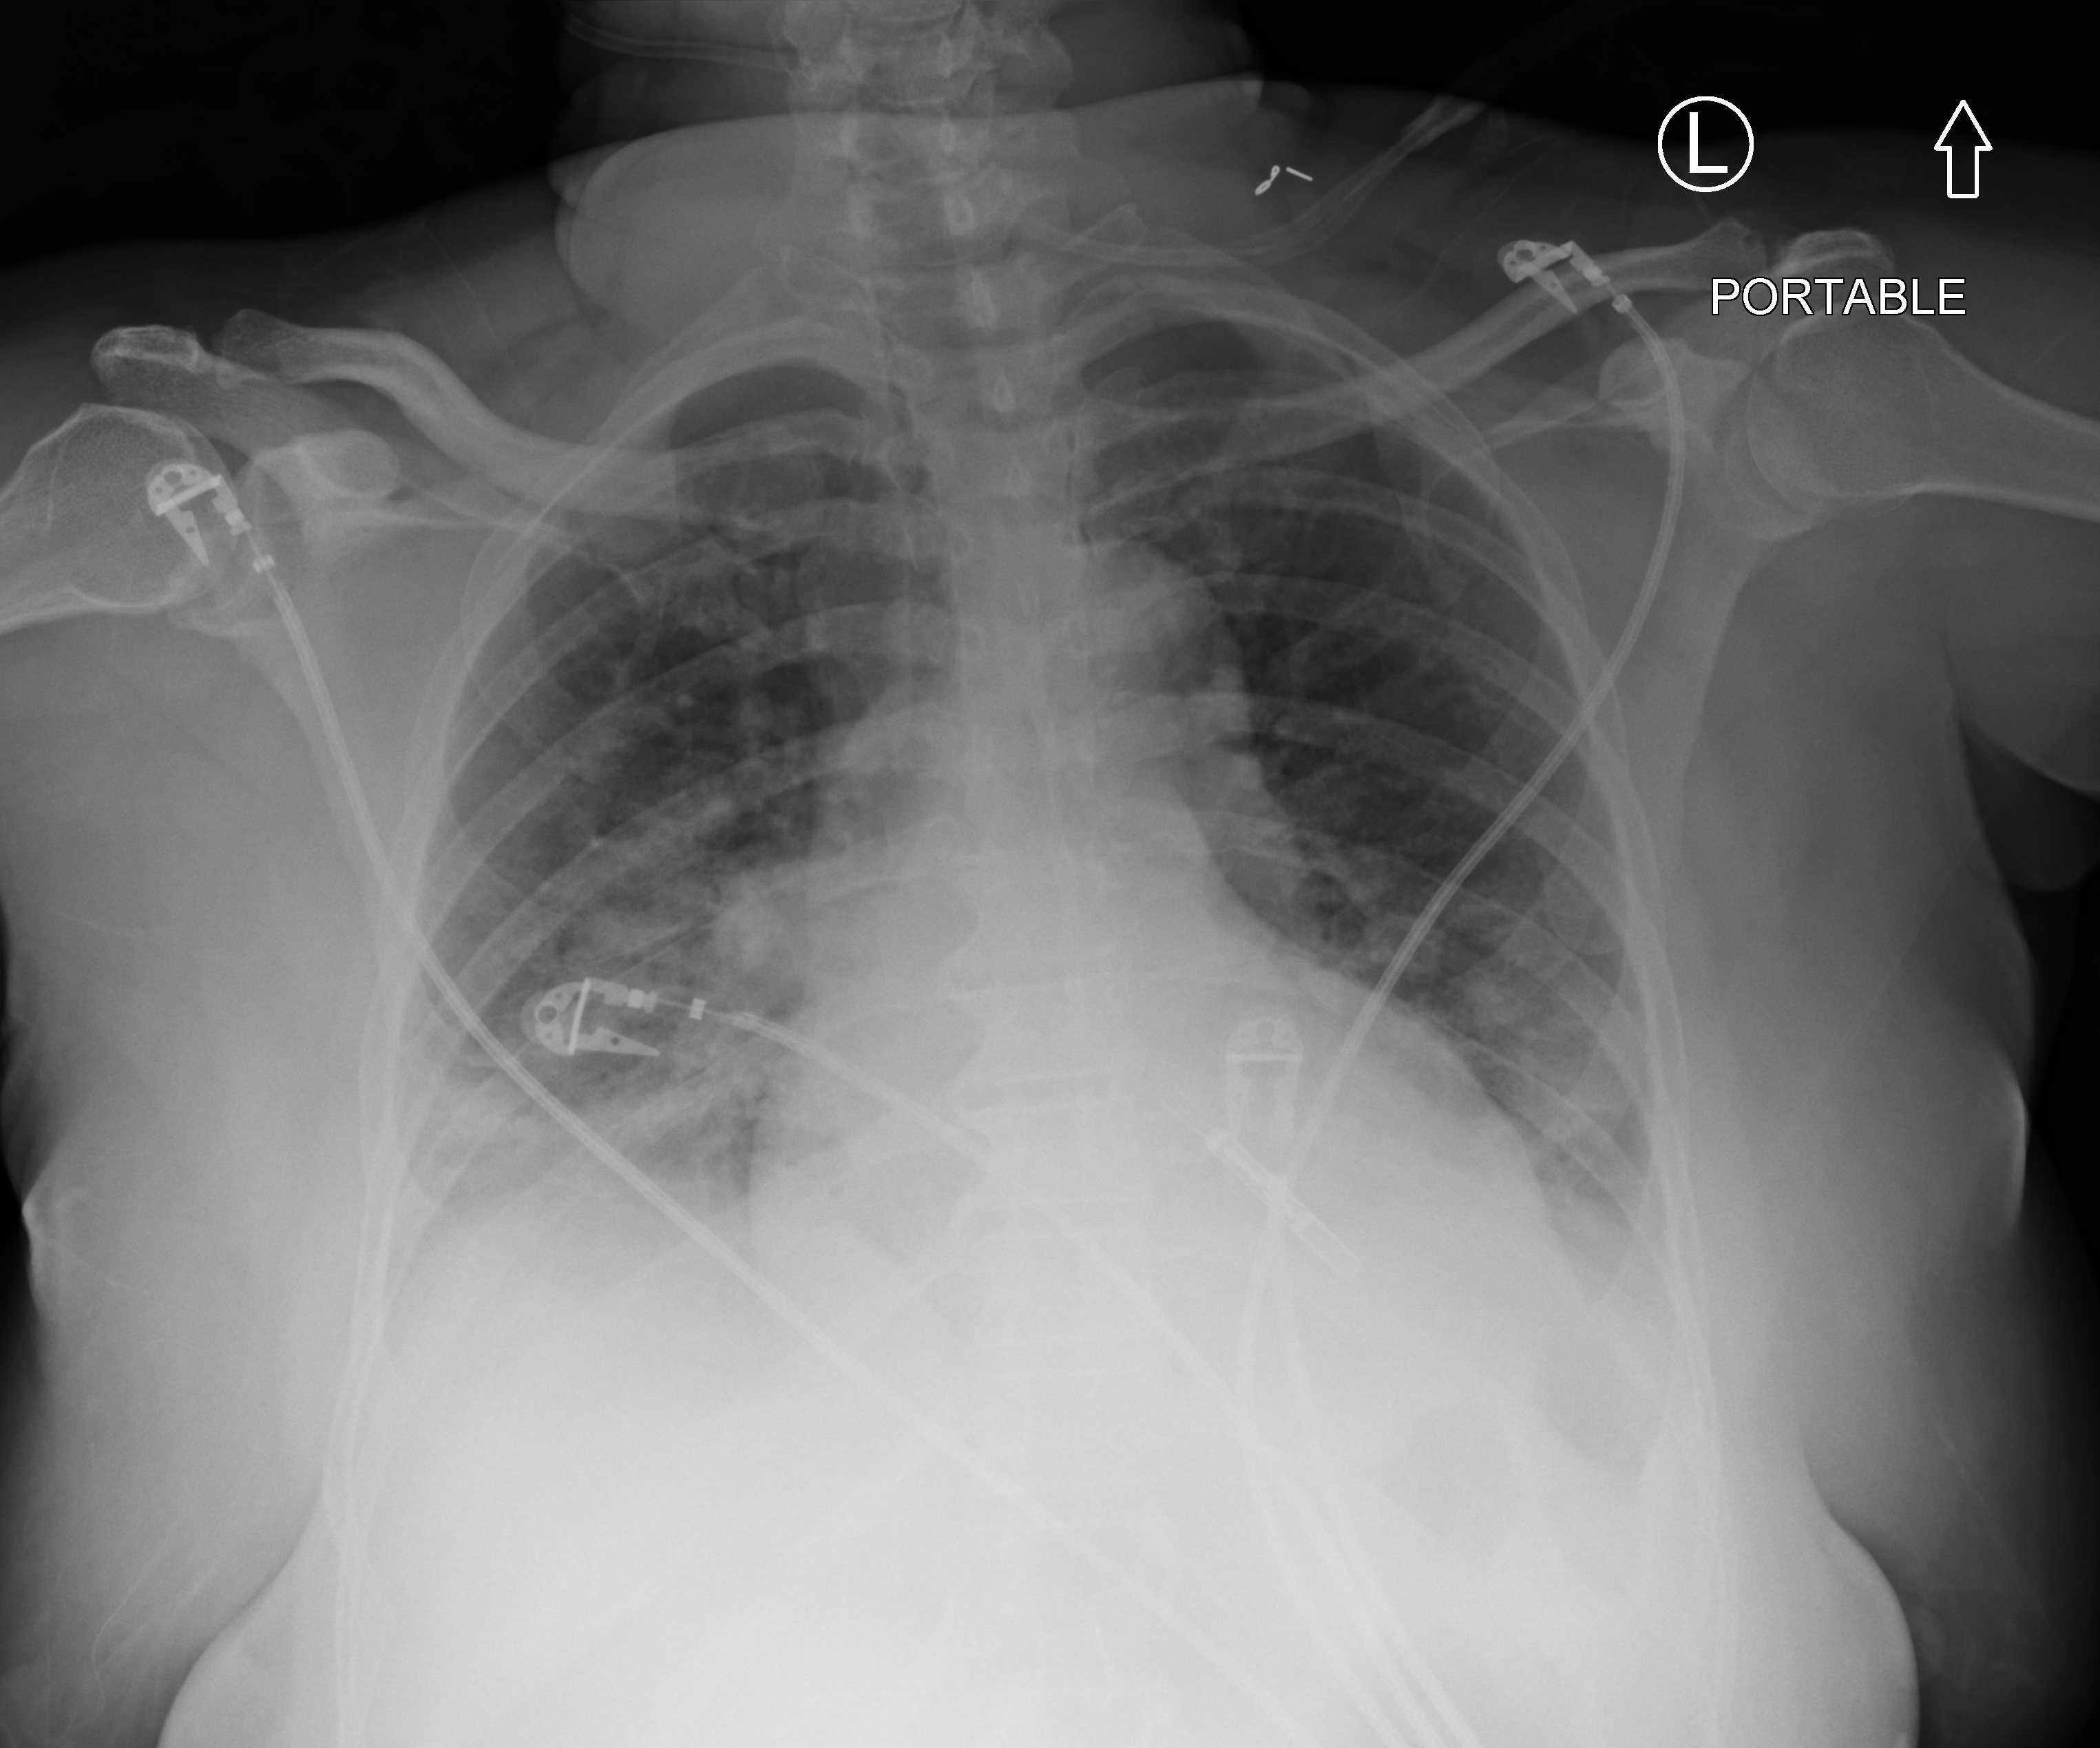
Bedside chest radiograph (computed radiography); anteroposterior (AP) projection. Female patient hospitalised with COVID-19, age 18–59 years.
Hospital-stay facts (about this admission, not read from this image; timing relative to this image not recorded): admitted to intensive care during this hospital stay: no; mechanically ventilated during this hospital stay: no.